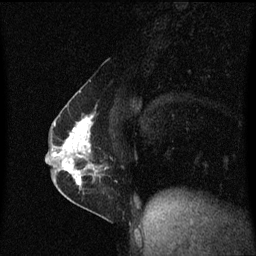
Breast MRI (dynamic contrast-enhanced), one sagittal slice. Slice 29 of 60 in the series (ordered by position). Dynamic contrast-enhanced series, image 2 of 3 at this slice position (ordered by acquisition). 1.5 T. TE 4.2 ms, TR 8.4 ms. 2 mm slice thickness. 256 × 256 image matrix, field of view 200 × 200 mm. Female patient, age 40 years.
Outlined on this slice (semi-automatic segmentation, software-assisted and operator-edited):
- analysis volume of interest (the breast-tissue region the enhancement analysis was run in; not a lesion): box from (x=57, y=110) to (x=105, y=191) px
- tumour enhancement mask (voxels above the 70 % enhancement threshold inside the analysis volume of interest): (x=62, y=114)–(x=97, y=187)